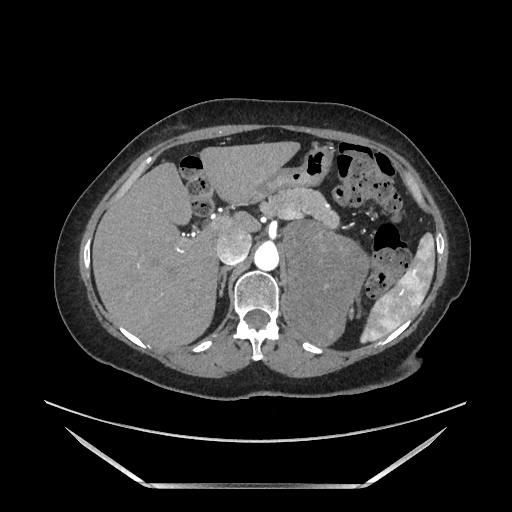
Contrast-enhanced abdominal CT, one axial slice. Slice 120 of 205 in the series (ordered by position). Soft-tissue window (W 400 / L 40 HU). 512 × 512 image matrix. Female patient. Case-level facts recorded for this patient, not image findings: diagnosis: adrenocortical carcinoma; tumour side: left adrenal; tumour size at pathology: 12.5 cm; Ki-67 index: 39 %; stage (as recorded): 3.
Structures marked on this image (semi-automatic segmentation, software-assisted and operator-edited):
- mass: bounding box [x1, y1, x2, y2] px = [285, 221, 368, 343]